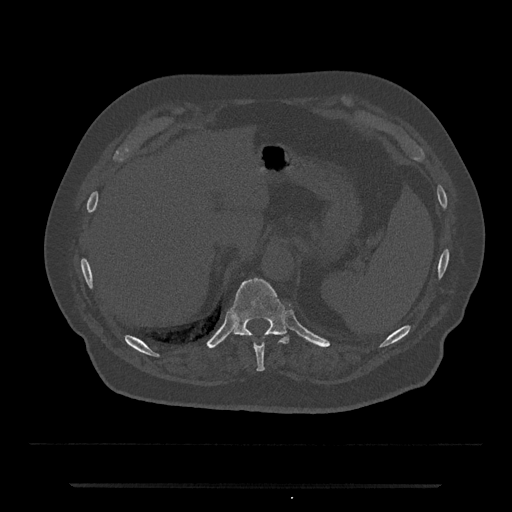
CT including the spine, one axial slice. Slice 670 of 797 in the series (ordered by position). Reconstruction kernel Br40s/3. Bone window (W 1800 / L 400 HU). 512 × 512 image matrix. Male patient, age 80 years. From the clinical record (not read from this slice): primary cancer: prostate; vertebrae with lytic lesions (as recorded): L1, T11.
Outlined on this slice (semi-automatic segmentation, software-assisted and operator-edited):
- T10 vertebra: bounding box [x1, y1, x2, y2] px = [253, 344, 265, 371]
- T11 vertebra: [231, 278, 292, 344]